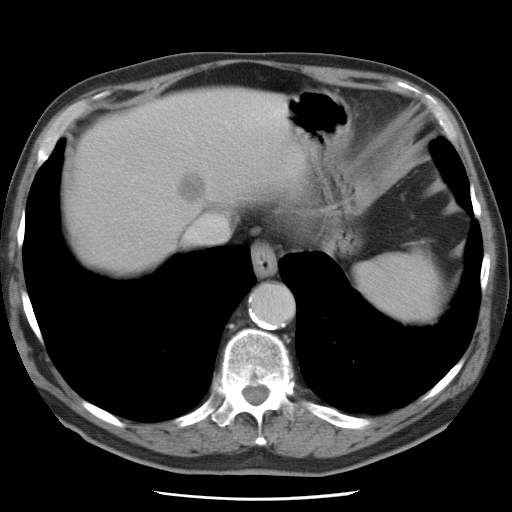
Contrast-enhanced abdominal CT, one axial slice. Position 68 of 78 along the scan axis. 120 kVp. Intravenous contrast given. Soft-tissue window (W 400 / L 40 HU). 5 mm slice thickness. 512 × 512 image matrix, field of view 337 × 337 mm. Male patient, age 75 years. From the clinical record (not read from this slice): diagnosis: colorectal cancer liver metastases, imaged before liver resection; multiple liver metastases: yes; largest metastasis: 2.4 cm; disease in both lobes: yes.
Annotated regions visible in this slice (outlined manually by an expert reader):
- hepatic veins: bounding box <186,123,227,241> (left, top, right, bottom; pixels)
- liver: <73,92,302,272>
- planned liver remnant (the part of the liver to remain after resection): <73,147,178,273>
- liver metastasis: <178,173,208,205>